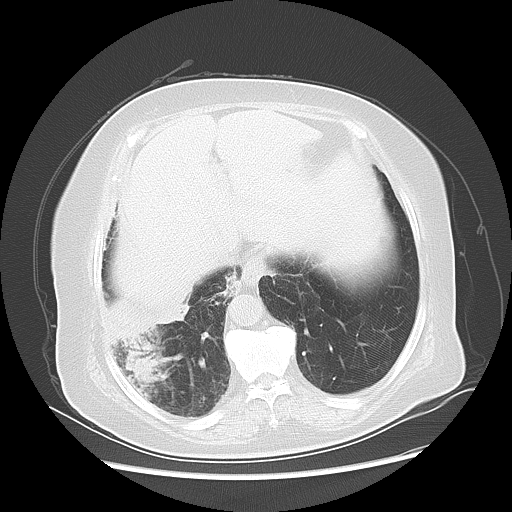
Chest CT, one axial slice; position 13 of 56 along the scan axis; reconstruction kernel LUNG; 120 kVp; lung window (W 1500 / L -600 HU); 5 mm slice thickness; 512 × 512 image matrix. Female patient, age 73 years. Case-level facts recorded for this patient, not image findings: clinical TNM (as recorded): T3 N0 M0.
Annotated regions visible in this slice (bounding box drawn by a radiologist):
- lung tumour (recorded histology: adenocarcinoma): box from (x=101, y=324) to (x=185, y=400) px